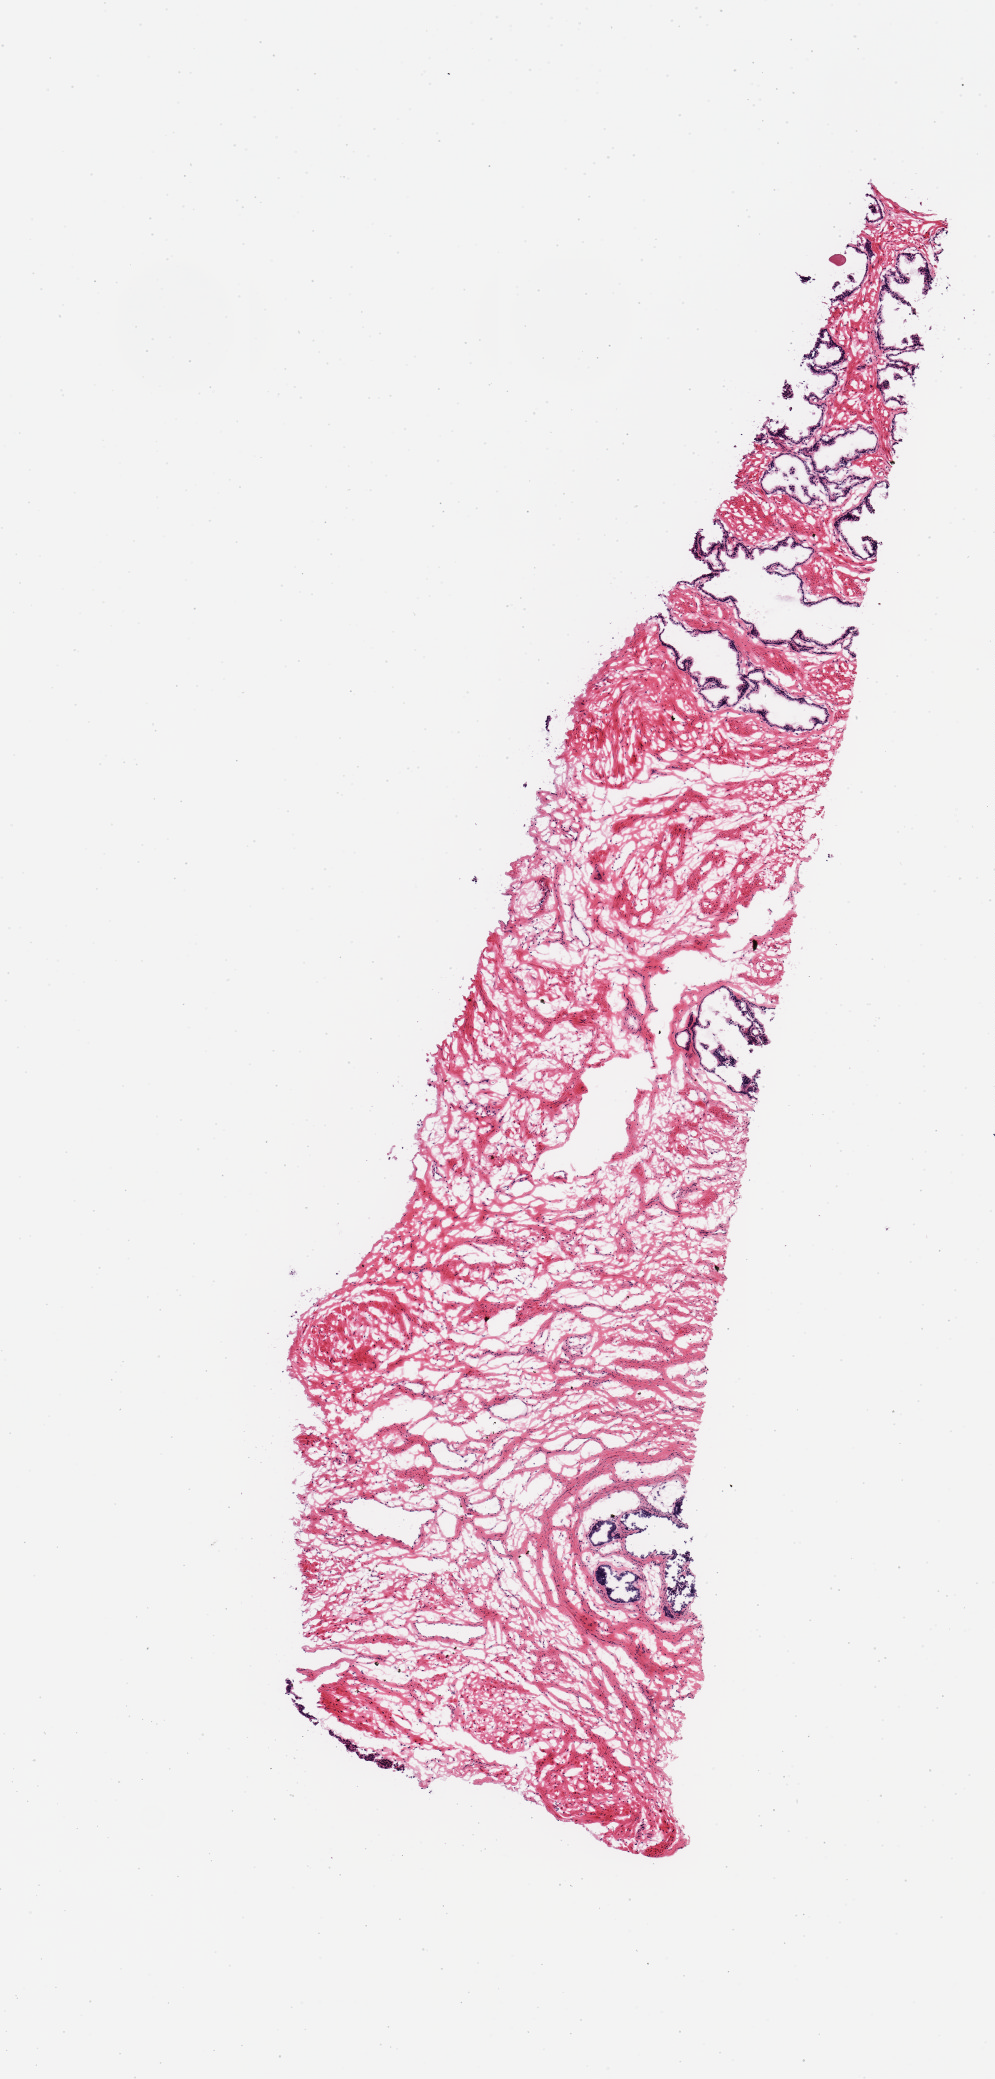
Hematoxylin and eosin (H&E) whole-slide image, brightfield — shown as a low-resolution overview of the whole scanned area (about 3.9 x 8.2 mm), frozen section, section of prostate (target tissue), tissue donor sample. Donor: male.
- pathologist's review note for this sample: 1 piece; comparable to PAXgene sample